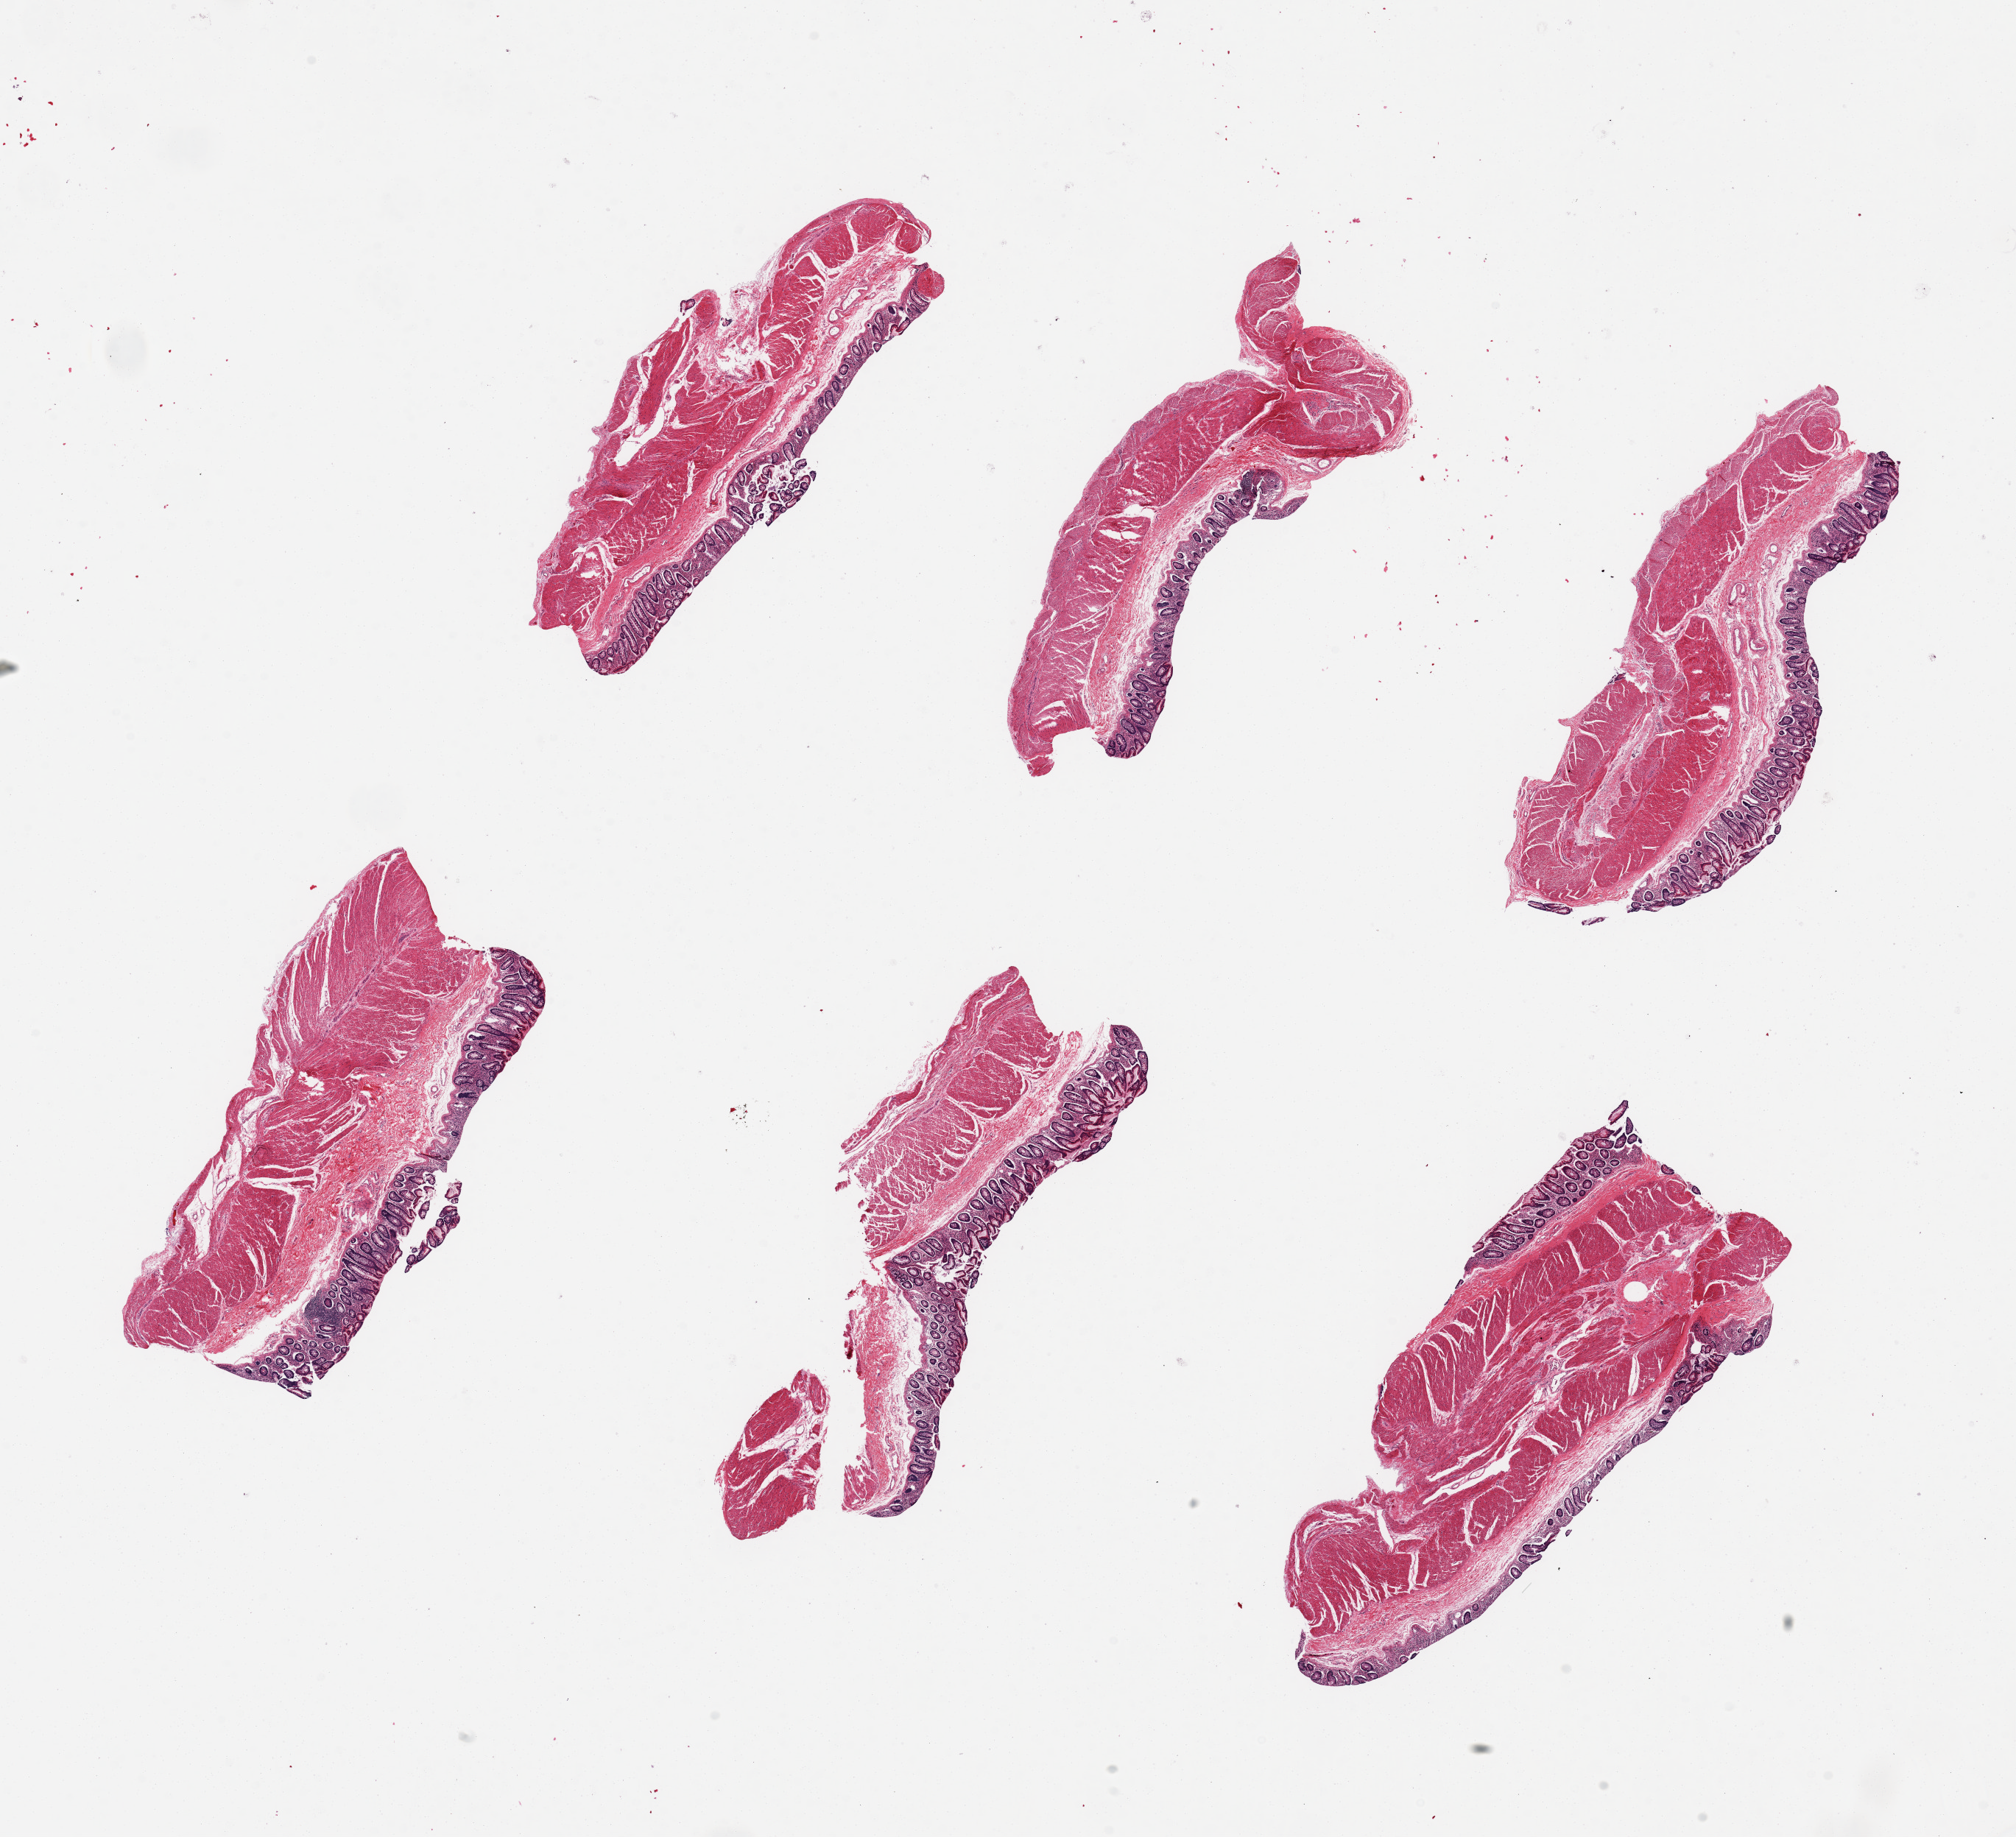
H&E whole-slide image, shown as a low-resolution overview of the whole scanned area (about 21.7 x 19.7 mm, slide scanned at 20x). PAXgene-fixed, paraffin-embedded tissue. Section of transverse colon (target tissue). Donor tissue sample. Donor sex: female.
* reviewer comment on this tissue sample: 6 pieces ~6x2.5mm. Mucosa unusually well-preserved, ~15-20% of thickness